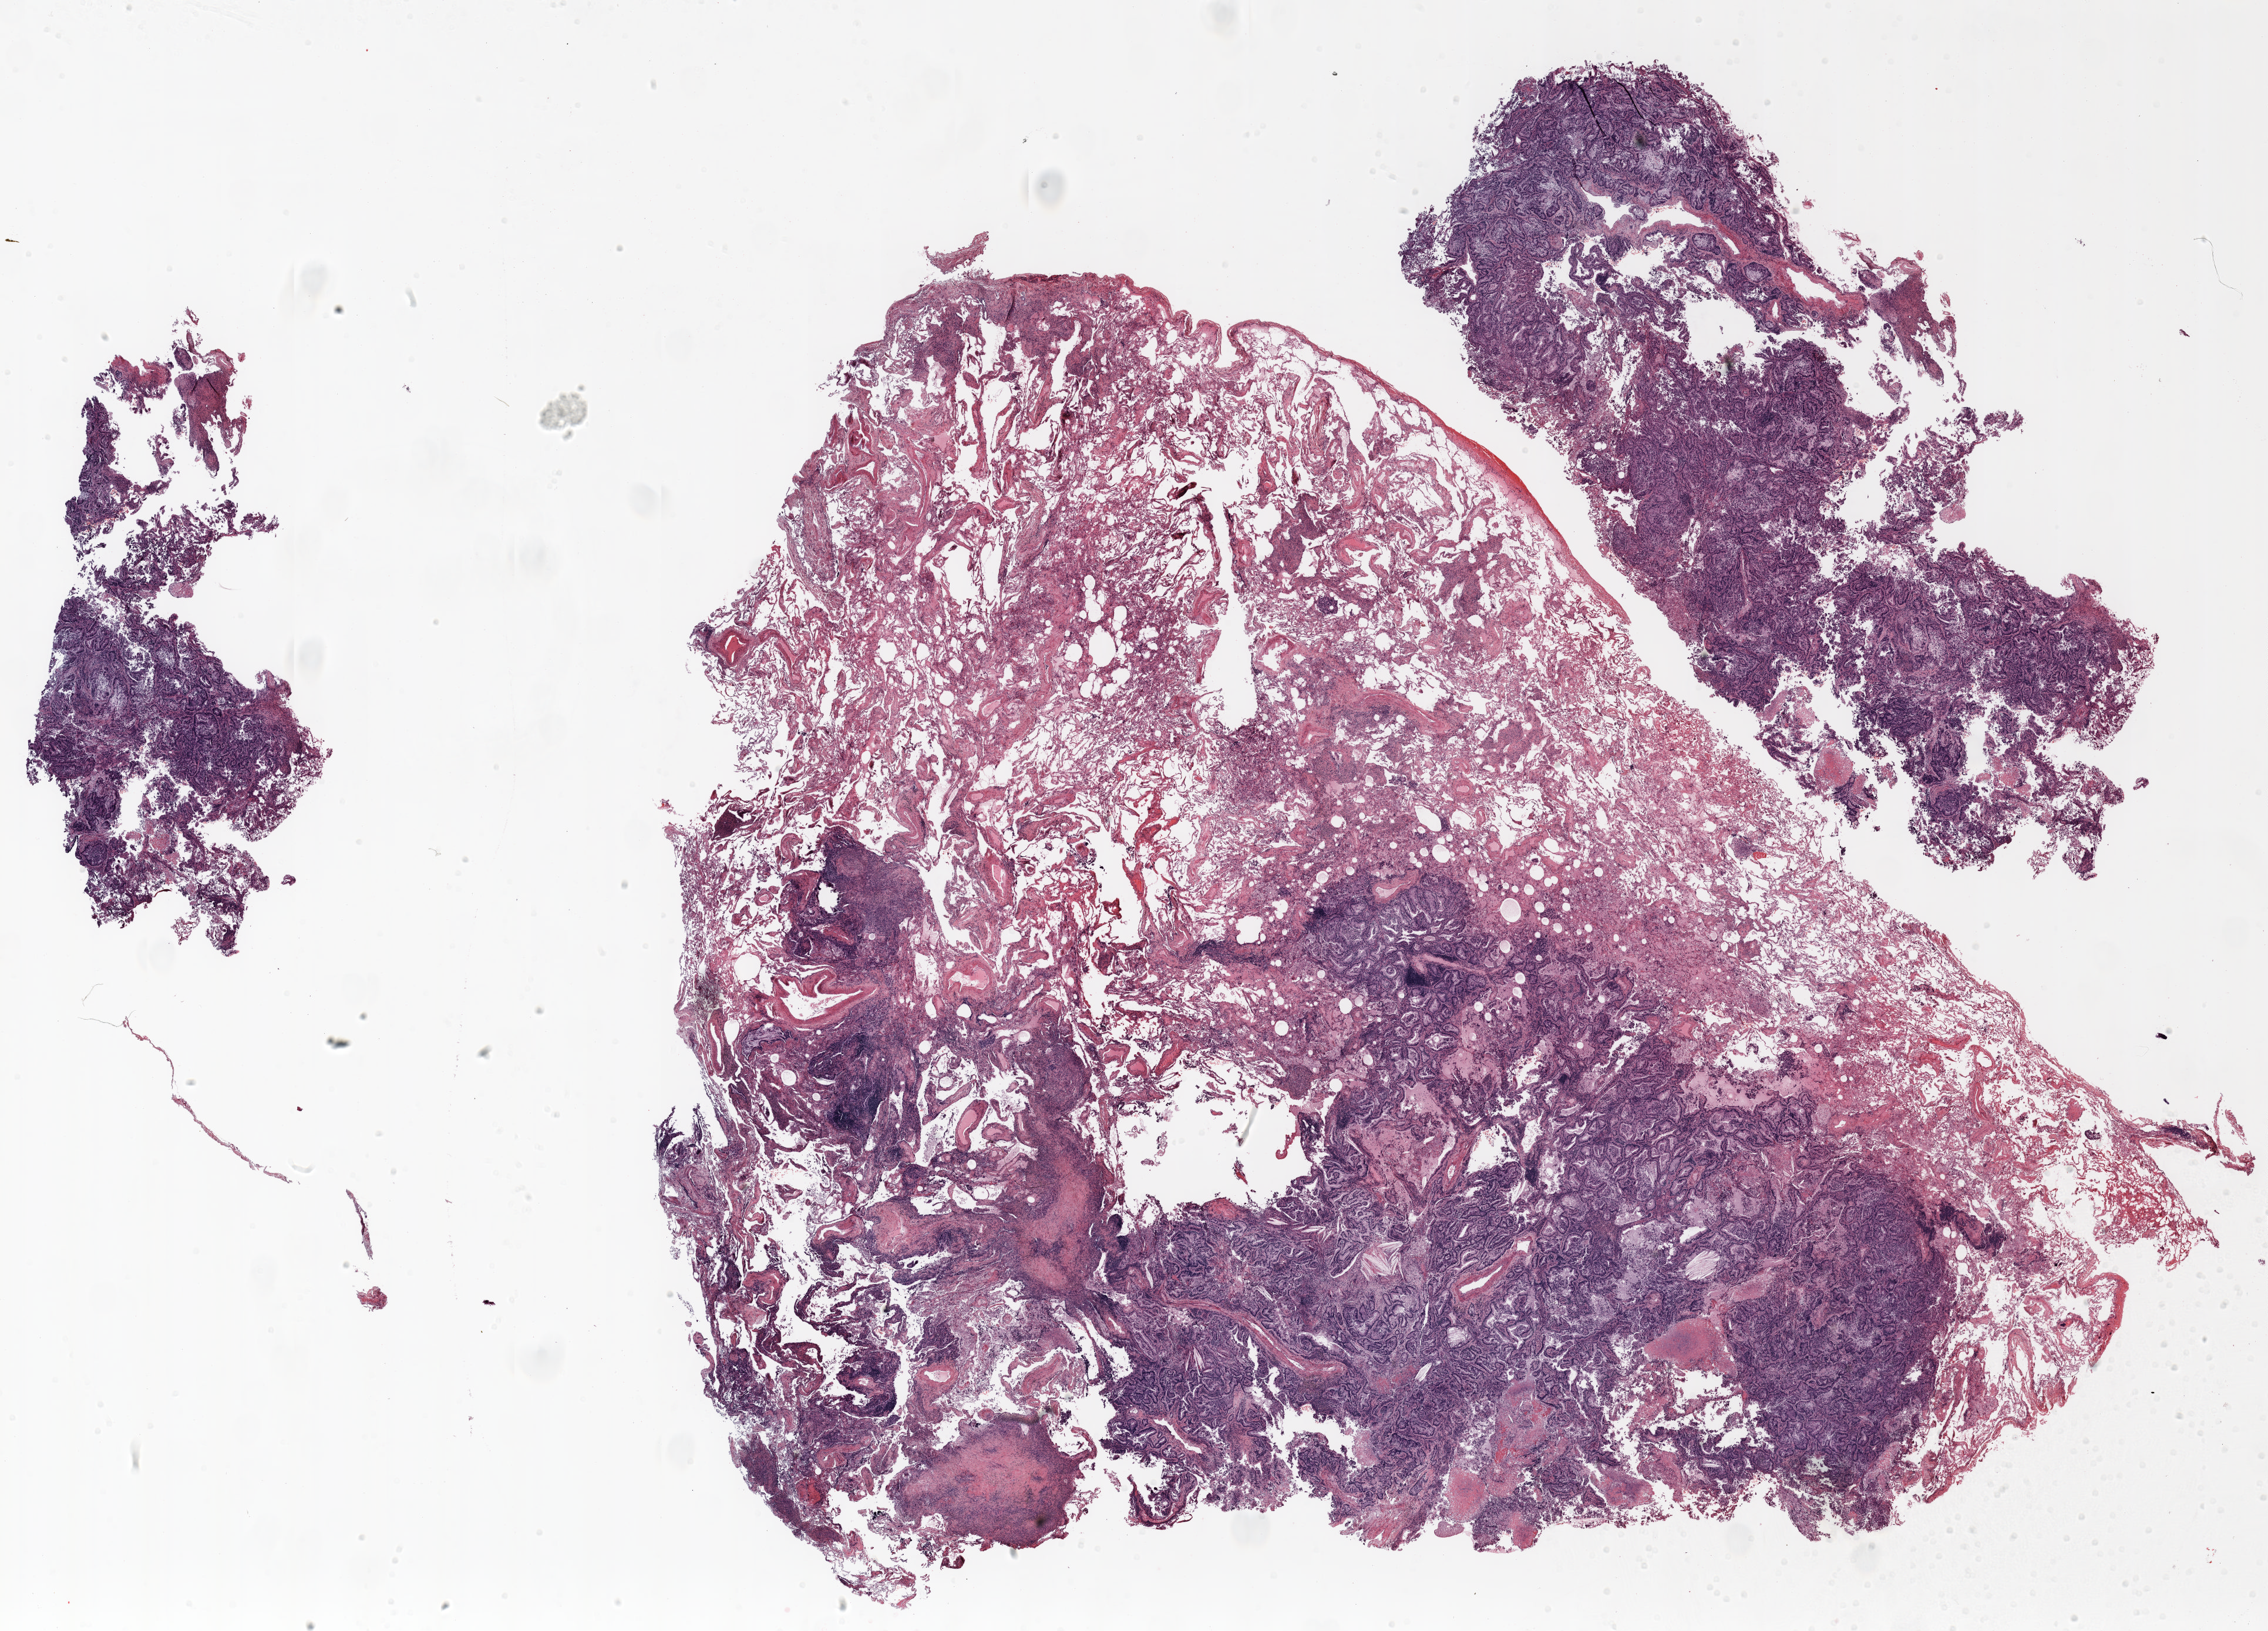
H&E whole-slide image — whole scanned area (about 31.0 x 22.3 mm) shown as a low-resolution overview, formalin-fixed paraffin-embedded (FFPE) section, lung tissue. Male, age 65 at enrolment. Former smoker at enrolment. Grade: moderately differentiated (G2).
Primary tumour location (clinical record): right upper lobe. Tumour size (pathology): 16 mm. Participant's lung-cancer diagnosis: Adenocarcinoma, NOS. Stage (AJCC 6th edition): IA.